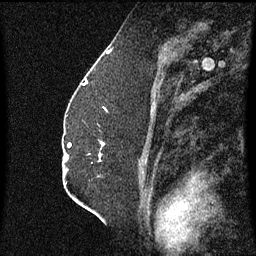
Breast MRI (dynamic contrast-enhanced), one sagittal slice. Slice 37 of 60 in the series (ordered by position). Dynamic contrast-enhanced series, image 2 of 3 at this slice position (ordered by acquisition). 1.5 T. TE 4.2 ms, TR 8.4 ms. 2.3 mm slice thickness. 256 × 256 image matrix. Female patient, age 52 years. Case-level facts recorded for this patient, not image findings: setting: breast cancer imaged before/during neoadjuvant chemotherapy; receptor status: HR-positive, HER2-negative.
Structures marked on this image (semi-automatic segmentation, software-assisted and operator-edited):
- analysis volume of interest (the breast-tissue region the enhancement analysis was run in; not a lesion): box from (x=98, y=142) to (x=104, y=163) px
- tumour enhancement mask (voxels above the 70 % enhancement threshold inside the analysis volume of interest): (x=99, y=144)–(x=104, y=161)